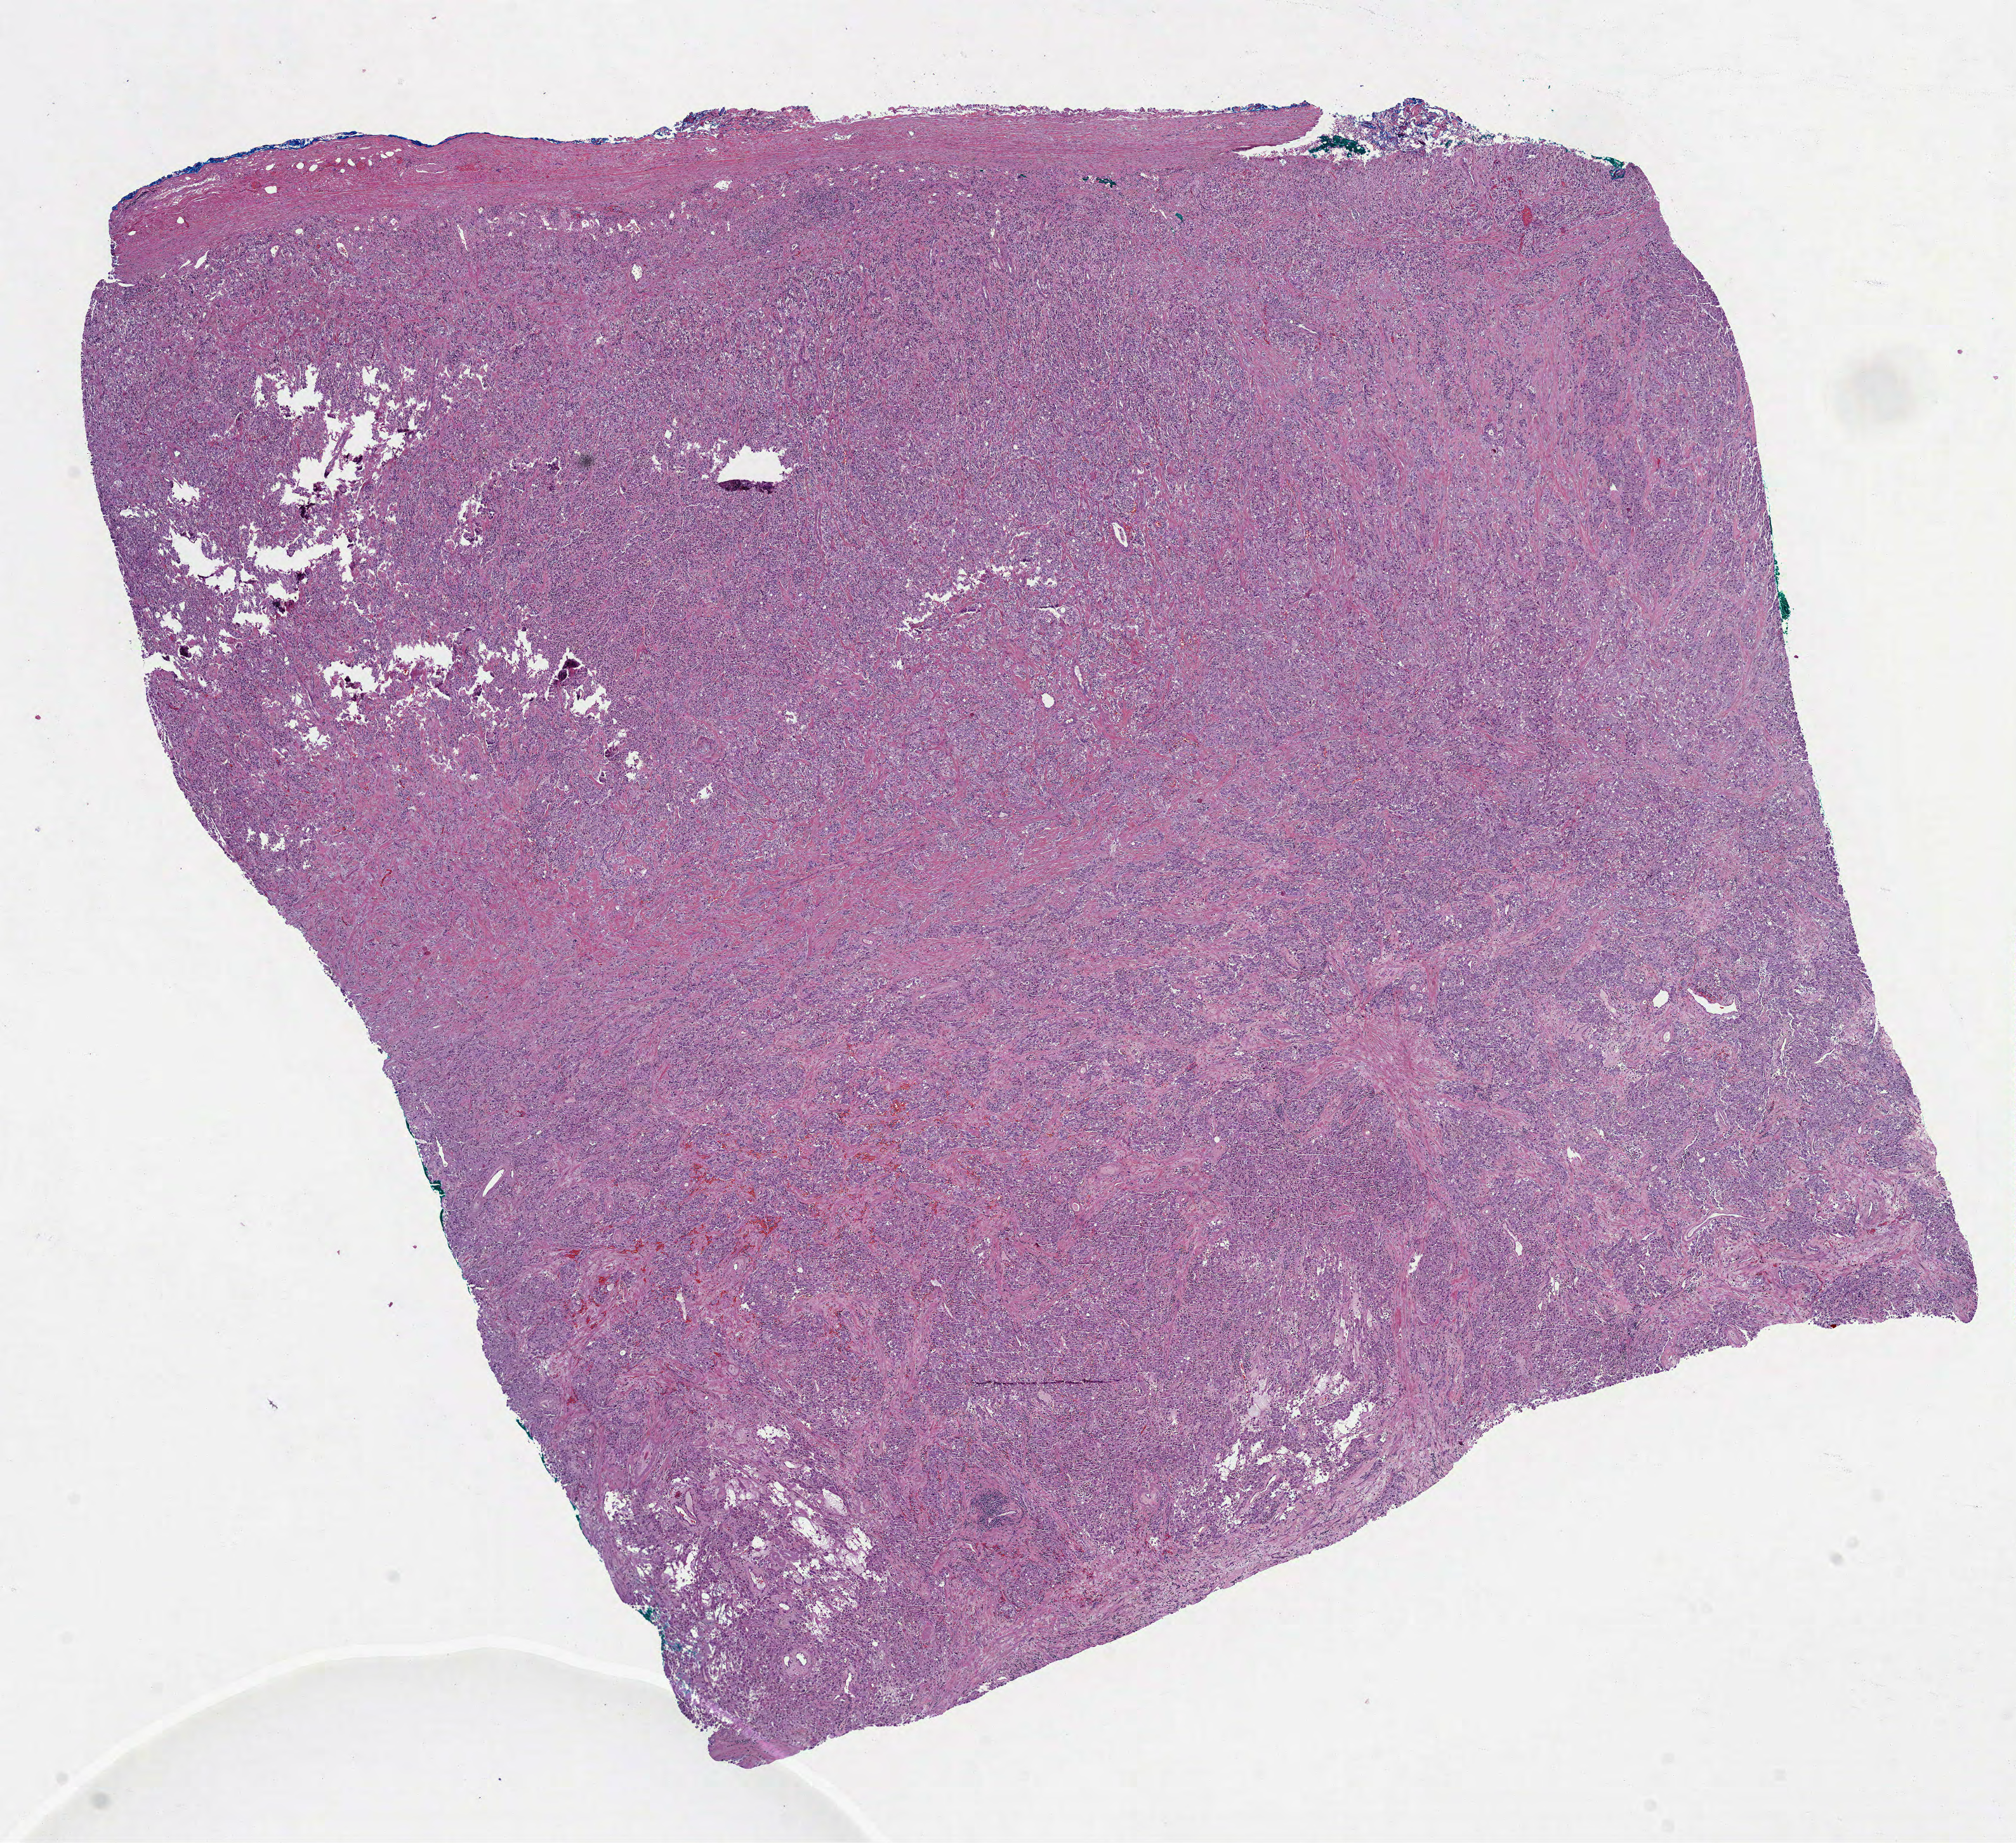
Hematoxylin and eosin (H&E) stained whole-slide image — whole scanned area (about 12.8 x 11.7 mm) shown as a low-resolution overview, FFPE section, primary tumour sample from the adrenal gland. Patient: male, age at initial diagnosis 53 years.
Histologic diagnosis: Pheochromocytoma, NOS.